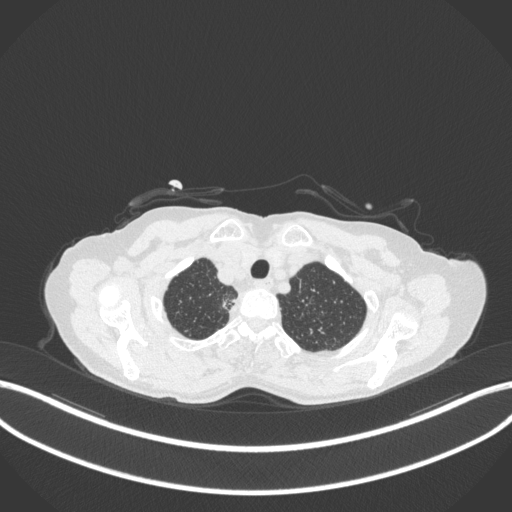
Chest CT, one axial slice. Slice 334 of 363 in the series (ordered by position). Lung window (W 1500 / L -600 HU). 1 mm slice thickness. 512 × 512 image matrix, field of view 400 × 400 mm. Patient: female, 75 years. Case-level facts recorded for this patient, not image findings: clinical TNM (as recorded): T1c N1 M1.
Annotated regions visible in this slice (bounding box drawn by a radiologist):
- lung tumour (recorded histology: adenocarcinoma): box from (x=213, y=288) to (x=242, y=314) px